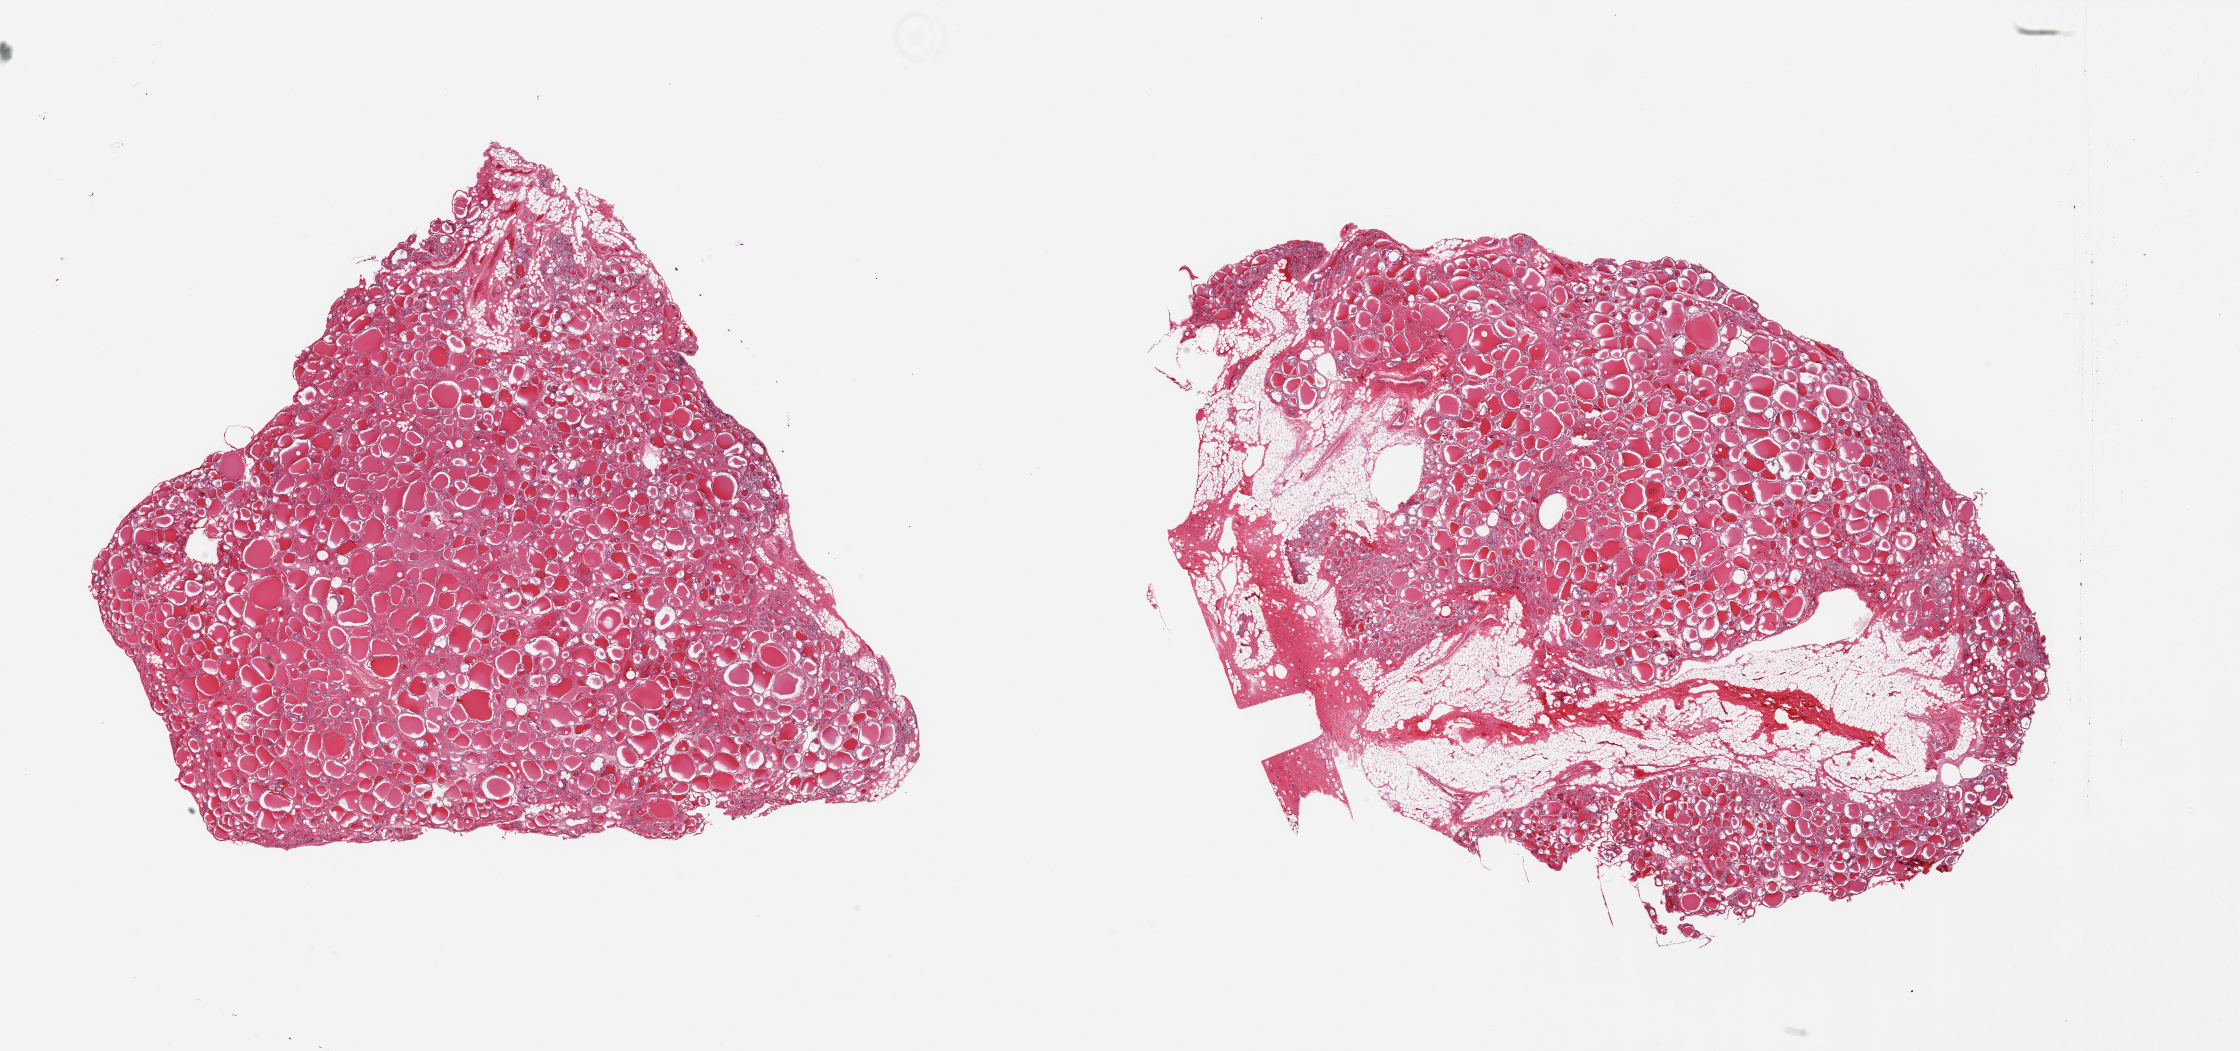
Whole-slide image, haematoxylin and eosin stain, brightfield — a low-resolution overview of the entire scanned area, about 35.4 x 16.6 mm; PAXgene-fixed paraffin-embedded (PFPE) section; section of thyroid (target tissue); donor tissue sample. Donor: male.
• pathologist's review note for this sample: 2 pieces, one section is ~30% adherent adjacent fat